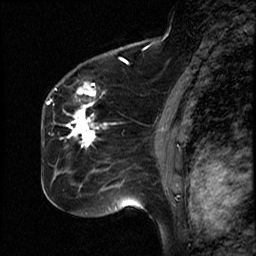
Breast MRI (dynamic contrast-enhanced), one sagittal slice; slice 33 of 50 in the series (ordered by position); dynamic contrast-enhanced study with each time point stored as its own series, time point 2 of 4 at this slice position (early post-contrast, ordered by acquisition time); 1.5 T; TE 4.2 ms, TR 18.5 ms; 3 mm slice thickness; 256 × 256 image matrix, field of view 200 × 200 mm. Patient: female, 44 years. From the clinical record (not read from this slice): setting: breast cancer imaged before/during neoadjuvant chemotherapy; receptor status: HR-positive, HER2-negative.
Annotated regions visible in this slice (semi-automatic segmentation, software-assisted and operator-edited):
- analysis volume of interest (the breast-tissue region the enhancement analysis was run in; not a lesion): box from (x=59, y=80) to (x=114, y=206) px
- tumour enhancement mask (voxels above the 100 % enhancement threshold inside the analysis volume of interest): (x=67, y=103)–(x=95, y=148)